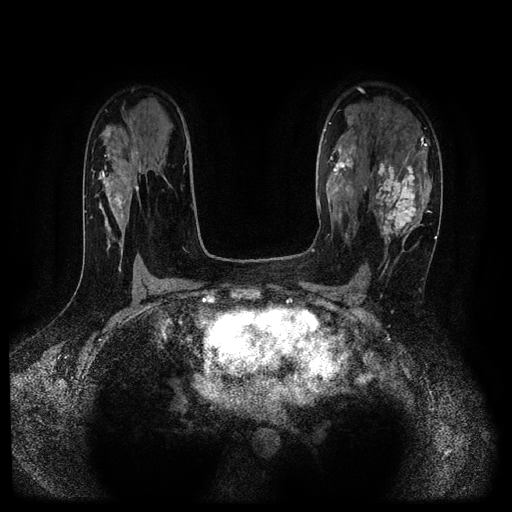
Breast MRI (dynamic contrast-enhanced, multi-phase), one axial slice; slice 68 of 116 in the series (ordered by position); dynamic contrast-enhanced series, time point 2 of 5 at this slice position (early post-contrast); 1.5 T; TE 2.7 ms, TR 5.4 ms; 512 × 512 image matrix, field of view 330 × 330 mm. Female patient, age 43 years.
Outlined on this slice (semi-automatically segmented with operator editing):
- breast lesion (labelled 'tumour' in the annotation; benign lesions carry a separate 'benign' label): bounding box [x1, y1, x2, y2] px = [369, 155, 422, 245]
- breast lesion (labelled benign in the annotation): [326, 146, 356, 196]